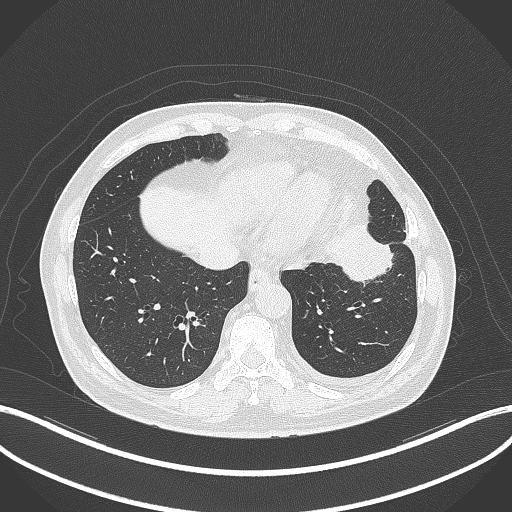
Chest CT, one axial slice; slice 97 of 230 in the series (ordered by position); lung window (W 1500 / L -600 HU); 1 mm slice thickness; 512 × 512 image matrix, field of view 400 × 400 mm. Patient: male, 68 years. Case-level facts recorded for this patient, not image findings: clinical TNM (as recorded): T2b N0 M0.
Outlined on this slice (bounding box drawn by a radiologist):
- lung tumour (recorded histology: squamous cell carcinoma): bounding box [x1, y1, x2, y2] px = [319, 217, 401, 292]